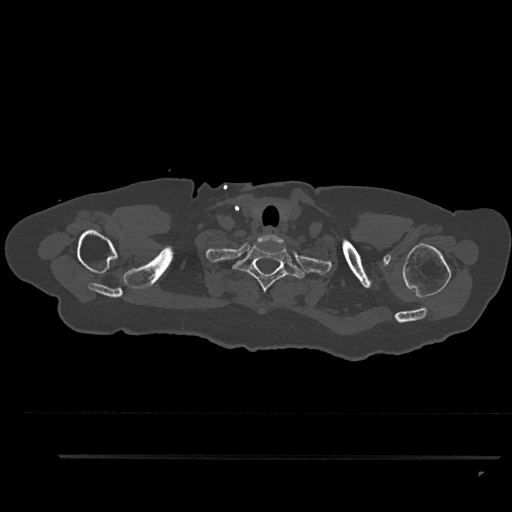
CT including the spine, one axial slice; position 765 of 797 along the scan axis; 120 kVp; bone window (W 1800 / L 400 HU); 0.5 mm slice thickness; 512 × 512 image matrix, field of view 408 × 408 mm. Female patient, age 44 years. From the clinical record (not read from this slice): primary cancer: renal; vertebrae with lytic lesions (as recorded): L1.
Structures marked on this image (semi-automatic segmentation, software-assisted and operator-edited):
- T1 vertebra: box from (x=232, y=246) to (x=306, y=292) px